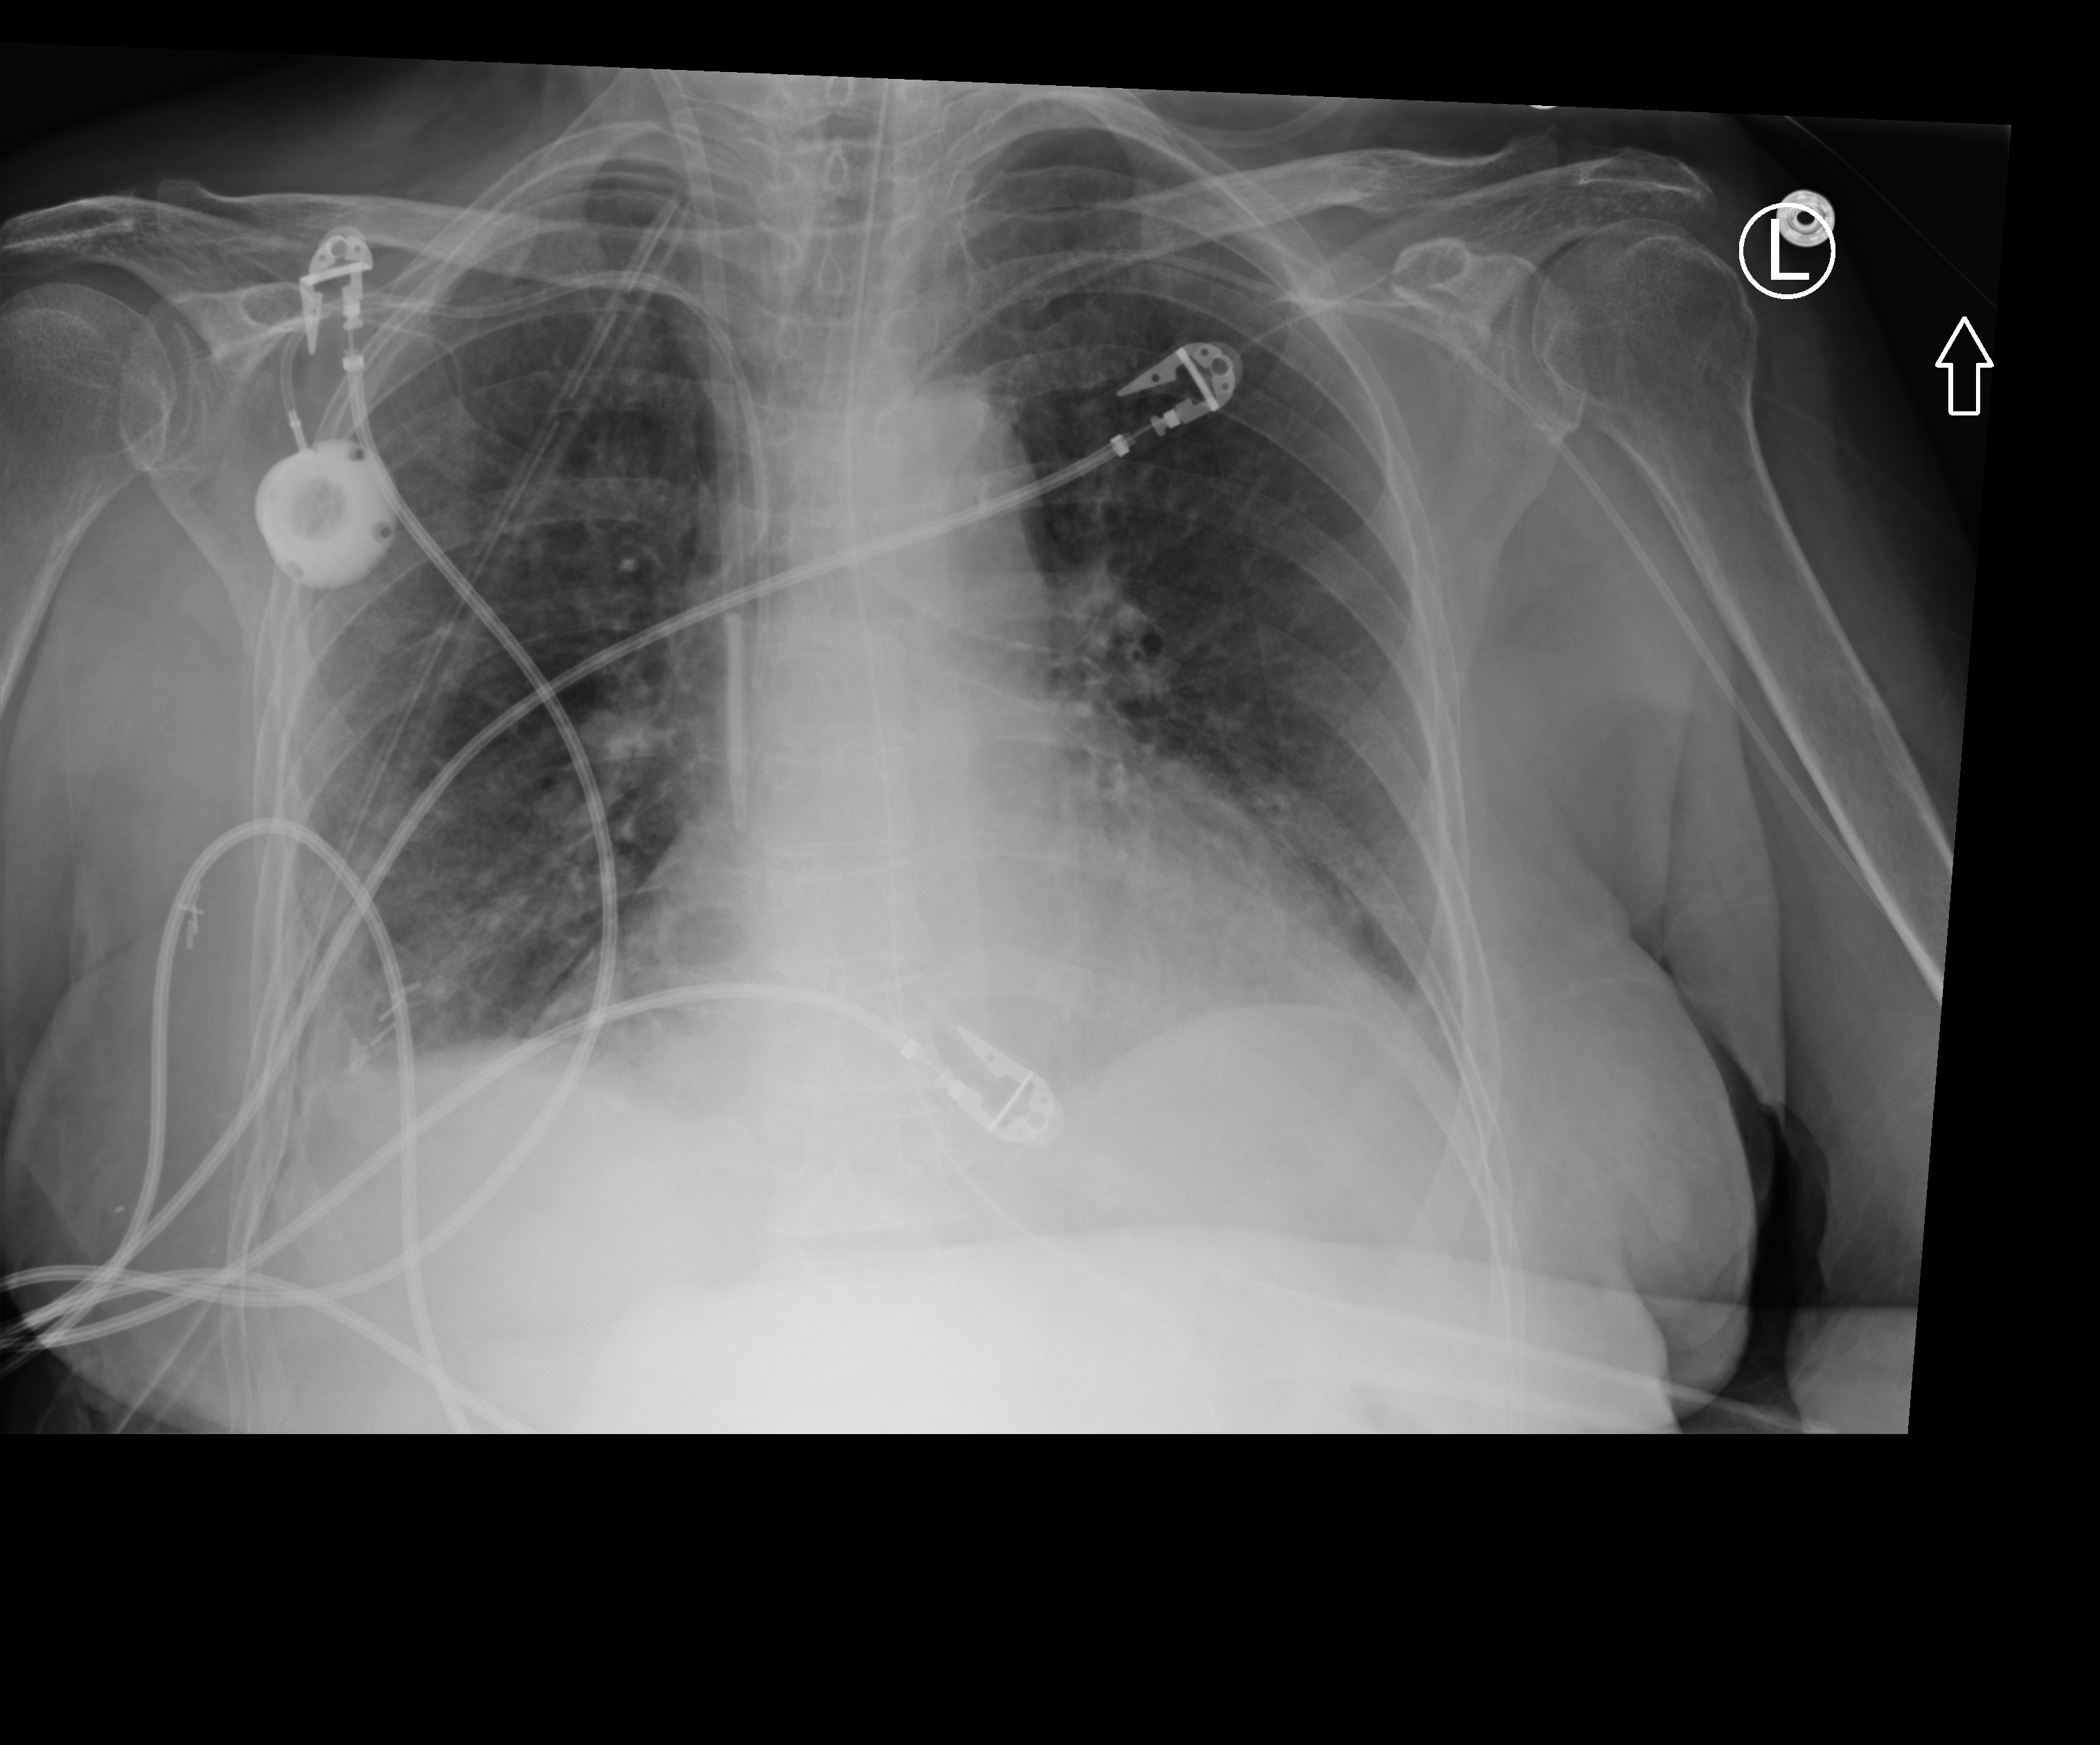
Chest X-ray (portable); anteroposterior (AP) projection. Patient hospitalised with COVID-19; female, aged 60–74 years.
From the hospital-stay record, not from the radiograph (when in the stay this image was taken is not recorded):
- mechanically ventilated during this hospital stay: yes